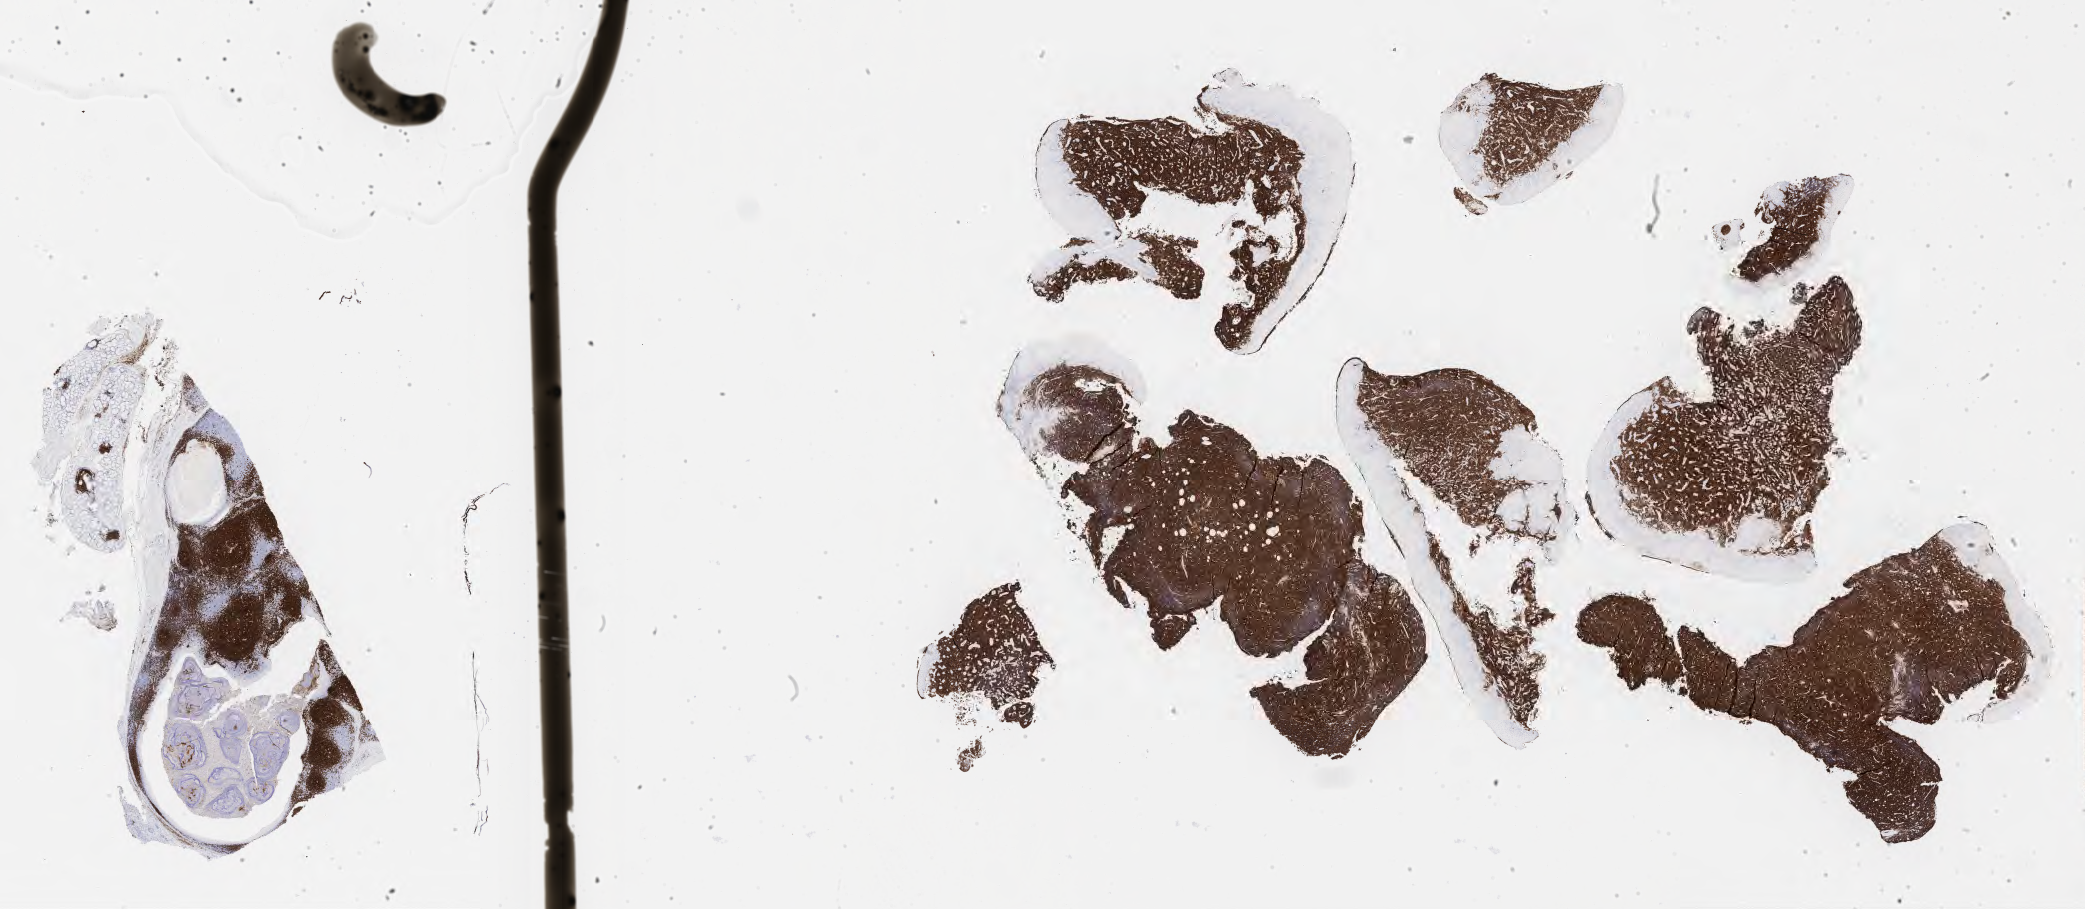
Immunohistochemistry (IHC) whole-slide image stained for CD20, shown as a low-resolution overview of the whole scanned area (about 33.7 x 14.7 mm). Tumor tissue. Patient male; aged 43.
Histologic diagnosis: Burkitt lymphoma, NOS.